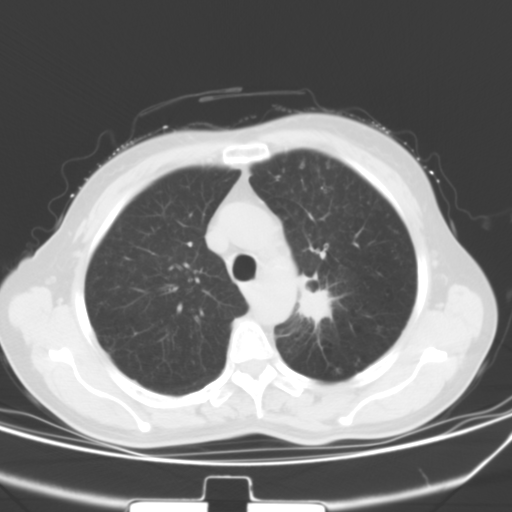
Chest CT, one axial slice; slice 42 of 53 in the series (ordered by position); 120 kVp; lung window (W 1500 / L -600 HU); 512 × 512 image matrix, field of view 329 × 329 mm. Patient: female, 60 years. Case-level facts recorded for this patient, not image findings: clinical TNM (as recorded): T1b N0 M0.
Structures marked on this image (rectangle marked by the reading radiologist):
- lung tumour (recorded histology: squamous cell carcinoma): bounding box [x1, y1, x2, y2] px = [295, 280, 328, 327]